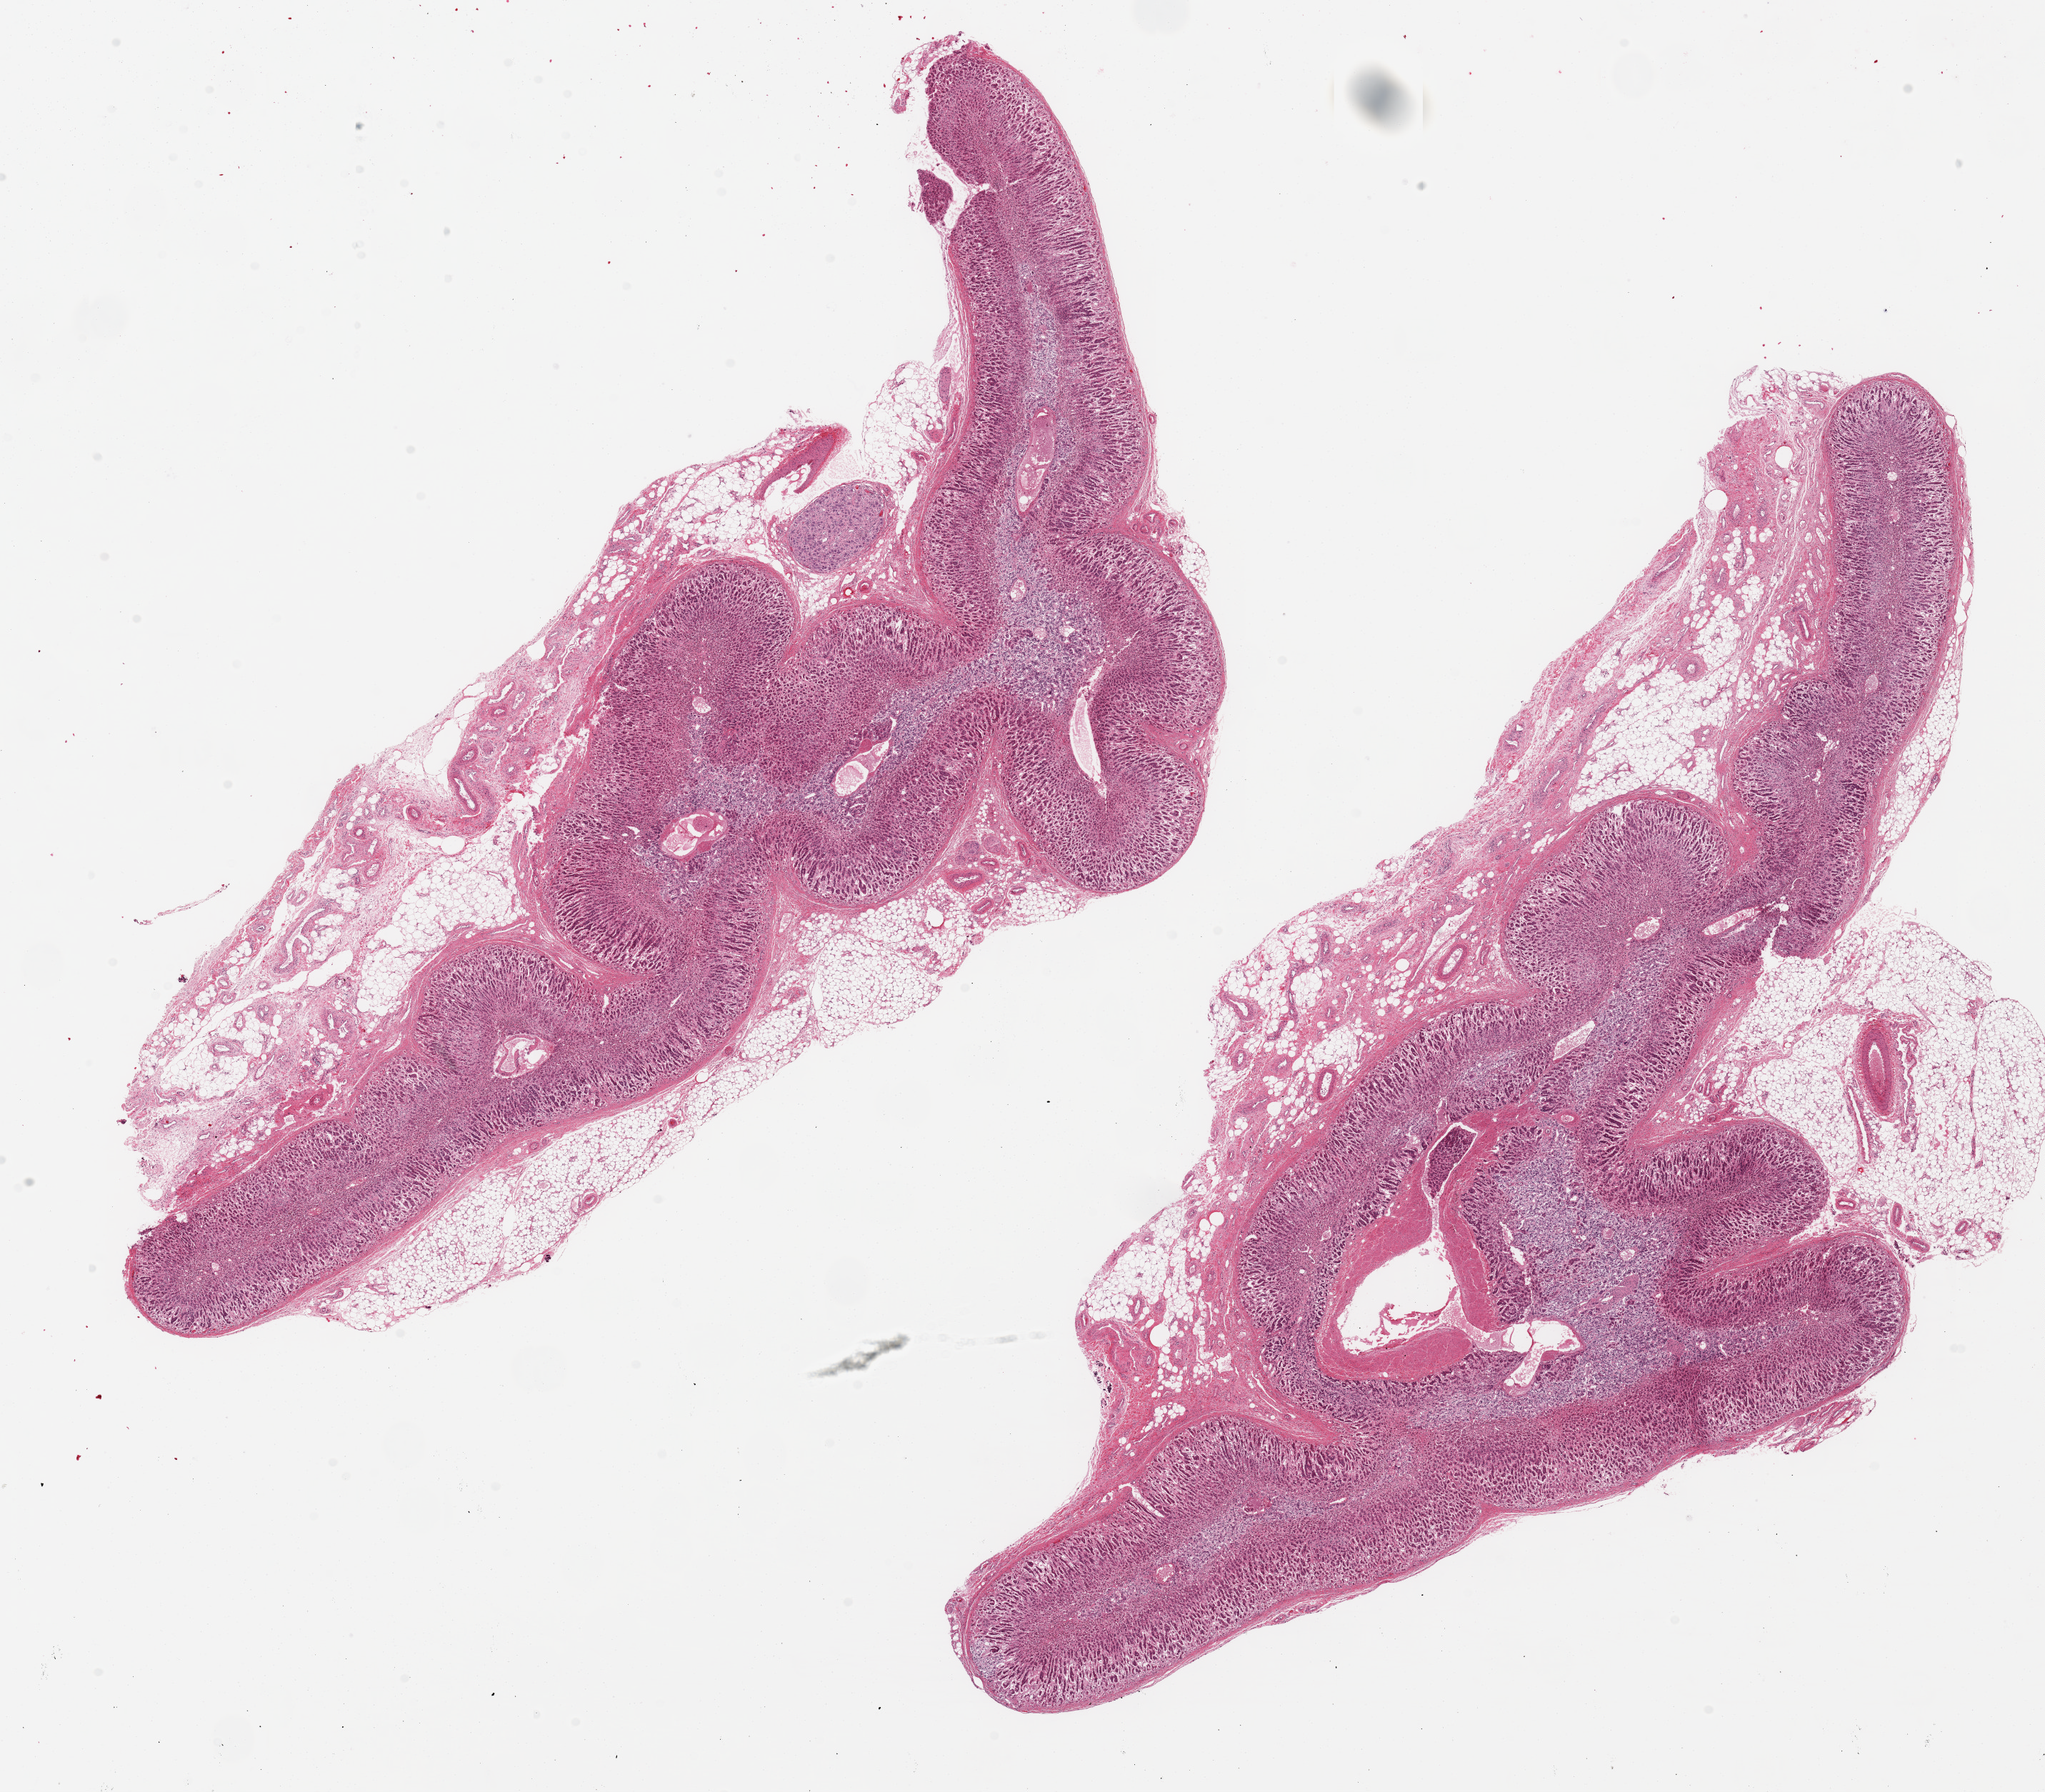
Digitized haematoxylin and eosin-stained section — whole scanned area (about 22.6 x 19.8 mm, from a 20x scan) shown as a low-resolution overview; PAXgene-fixed, paraffin-embedded tissue; sampled site (target tissue): adrenal gland; tissue donor sample. Female donor.
- review note (as recorded): 2 ~17x8mm aliquots, each with a 1-2mm rim of fat surrounding the majority of each